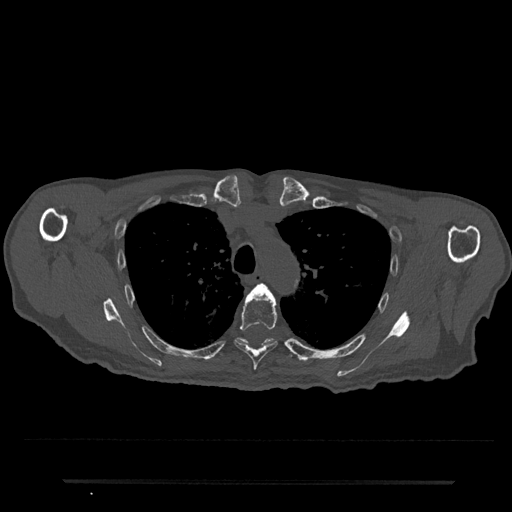
CT including the spine, one axial slice. Slice 574 of 797 in the series (ordered by position). 120 kVp. Bone window (W 1800 / L 400 HU). 0.5 mm slice thickness. 512 × 512 image matrix. Male patient, age 74 years. From the clinical record (not read from this slice): primary cancer: prostate.
Outlined on this slice (semi-automatic segmentation, software-assisted and operator-edited):
- T4 vertebra: box from (x=250, y=283) to (x=271, y=295) px
- T5 vertebra: (x=234, y=290)–(x=278, y=370)
- T6 vertebra: (x=219, y=338)–(x=295, y=356)